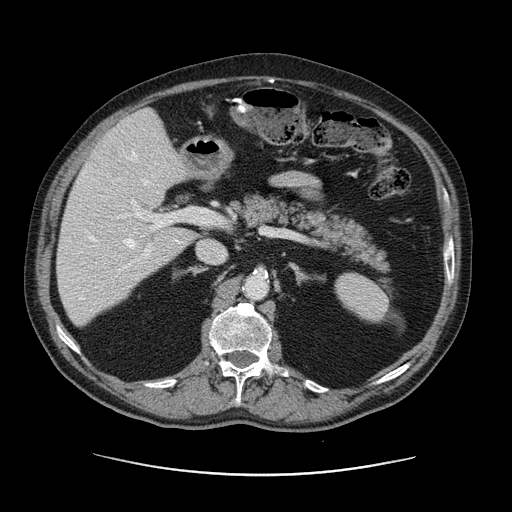
Contrast-enhanced abdominal CT, one axial slice. 120 kVp. Soft-tissue window (W 400 / L 40 HU). 512 × 512 image matrix, field of view 395 × 395 mm. Male patient, age 72 years. Case-level facts recorded for this patient, not image findings: diagnosis: colorectal cancer liver metastases, imaged before liver resection.
Outlined on this slice (manually delineated by an expert):
- hepatic veins: bounding box (x1, y1, x2, y2) in pixels: (89, 151, 148, 248)
- liver: (57, 110, 195, 326)
- planned liver remnant (the part of the liver to remain after resection): (57, 186, 195, 326)
- portal vein (with intrahepatic branches): (79, 199, 203, 300)